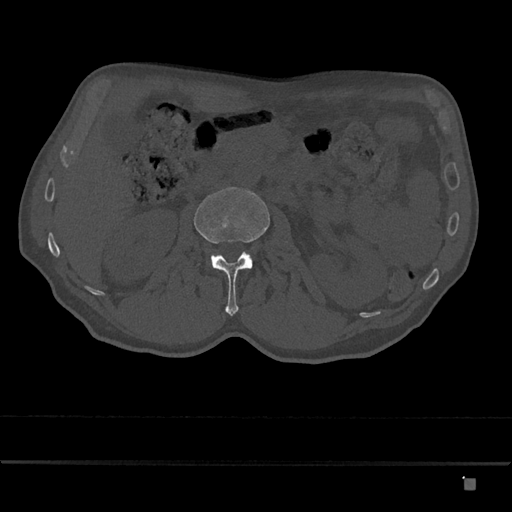
CT including the spine, one axial slice; position 466 of 797 along the scan axis; reconstruction kernel Br40s/3; bone window (W 1800 / L 400 HU); 512 × 512 image matrix, field of view 390 × 390 mm. Patient: male, 72 years. From the clinical record (not read from this slice): primary cancer: prostate.
Structures marked on this image (semi-automatically segmented with operator editing):
- L2 vertebra: bounding box <194,187,270,316> (left, top, right, bottom; pixels)